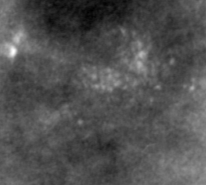
Region of interest cut from a scanned film mammogram (one marked finding); left breast; MLO view; BI-RADS breast density category 4 (scale 1–4).
Marked abnormality: calcifications, morphology pleomorphic, distribution clustered; BI-RADS assessment category 4; pathology result (as recorded, not read from the image): malignant.